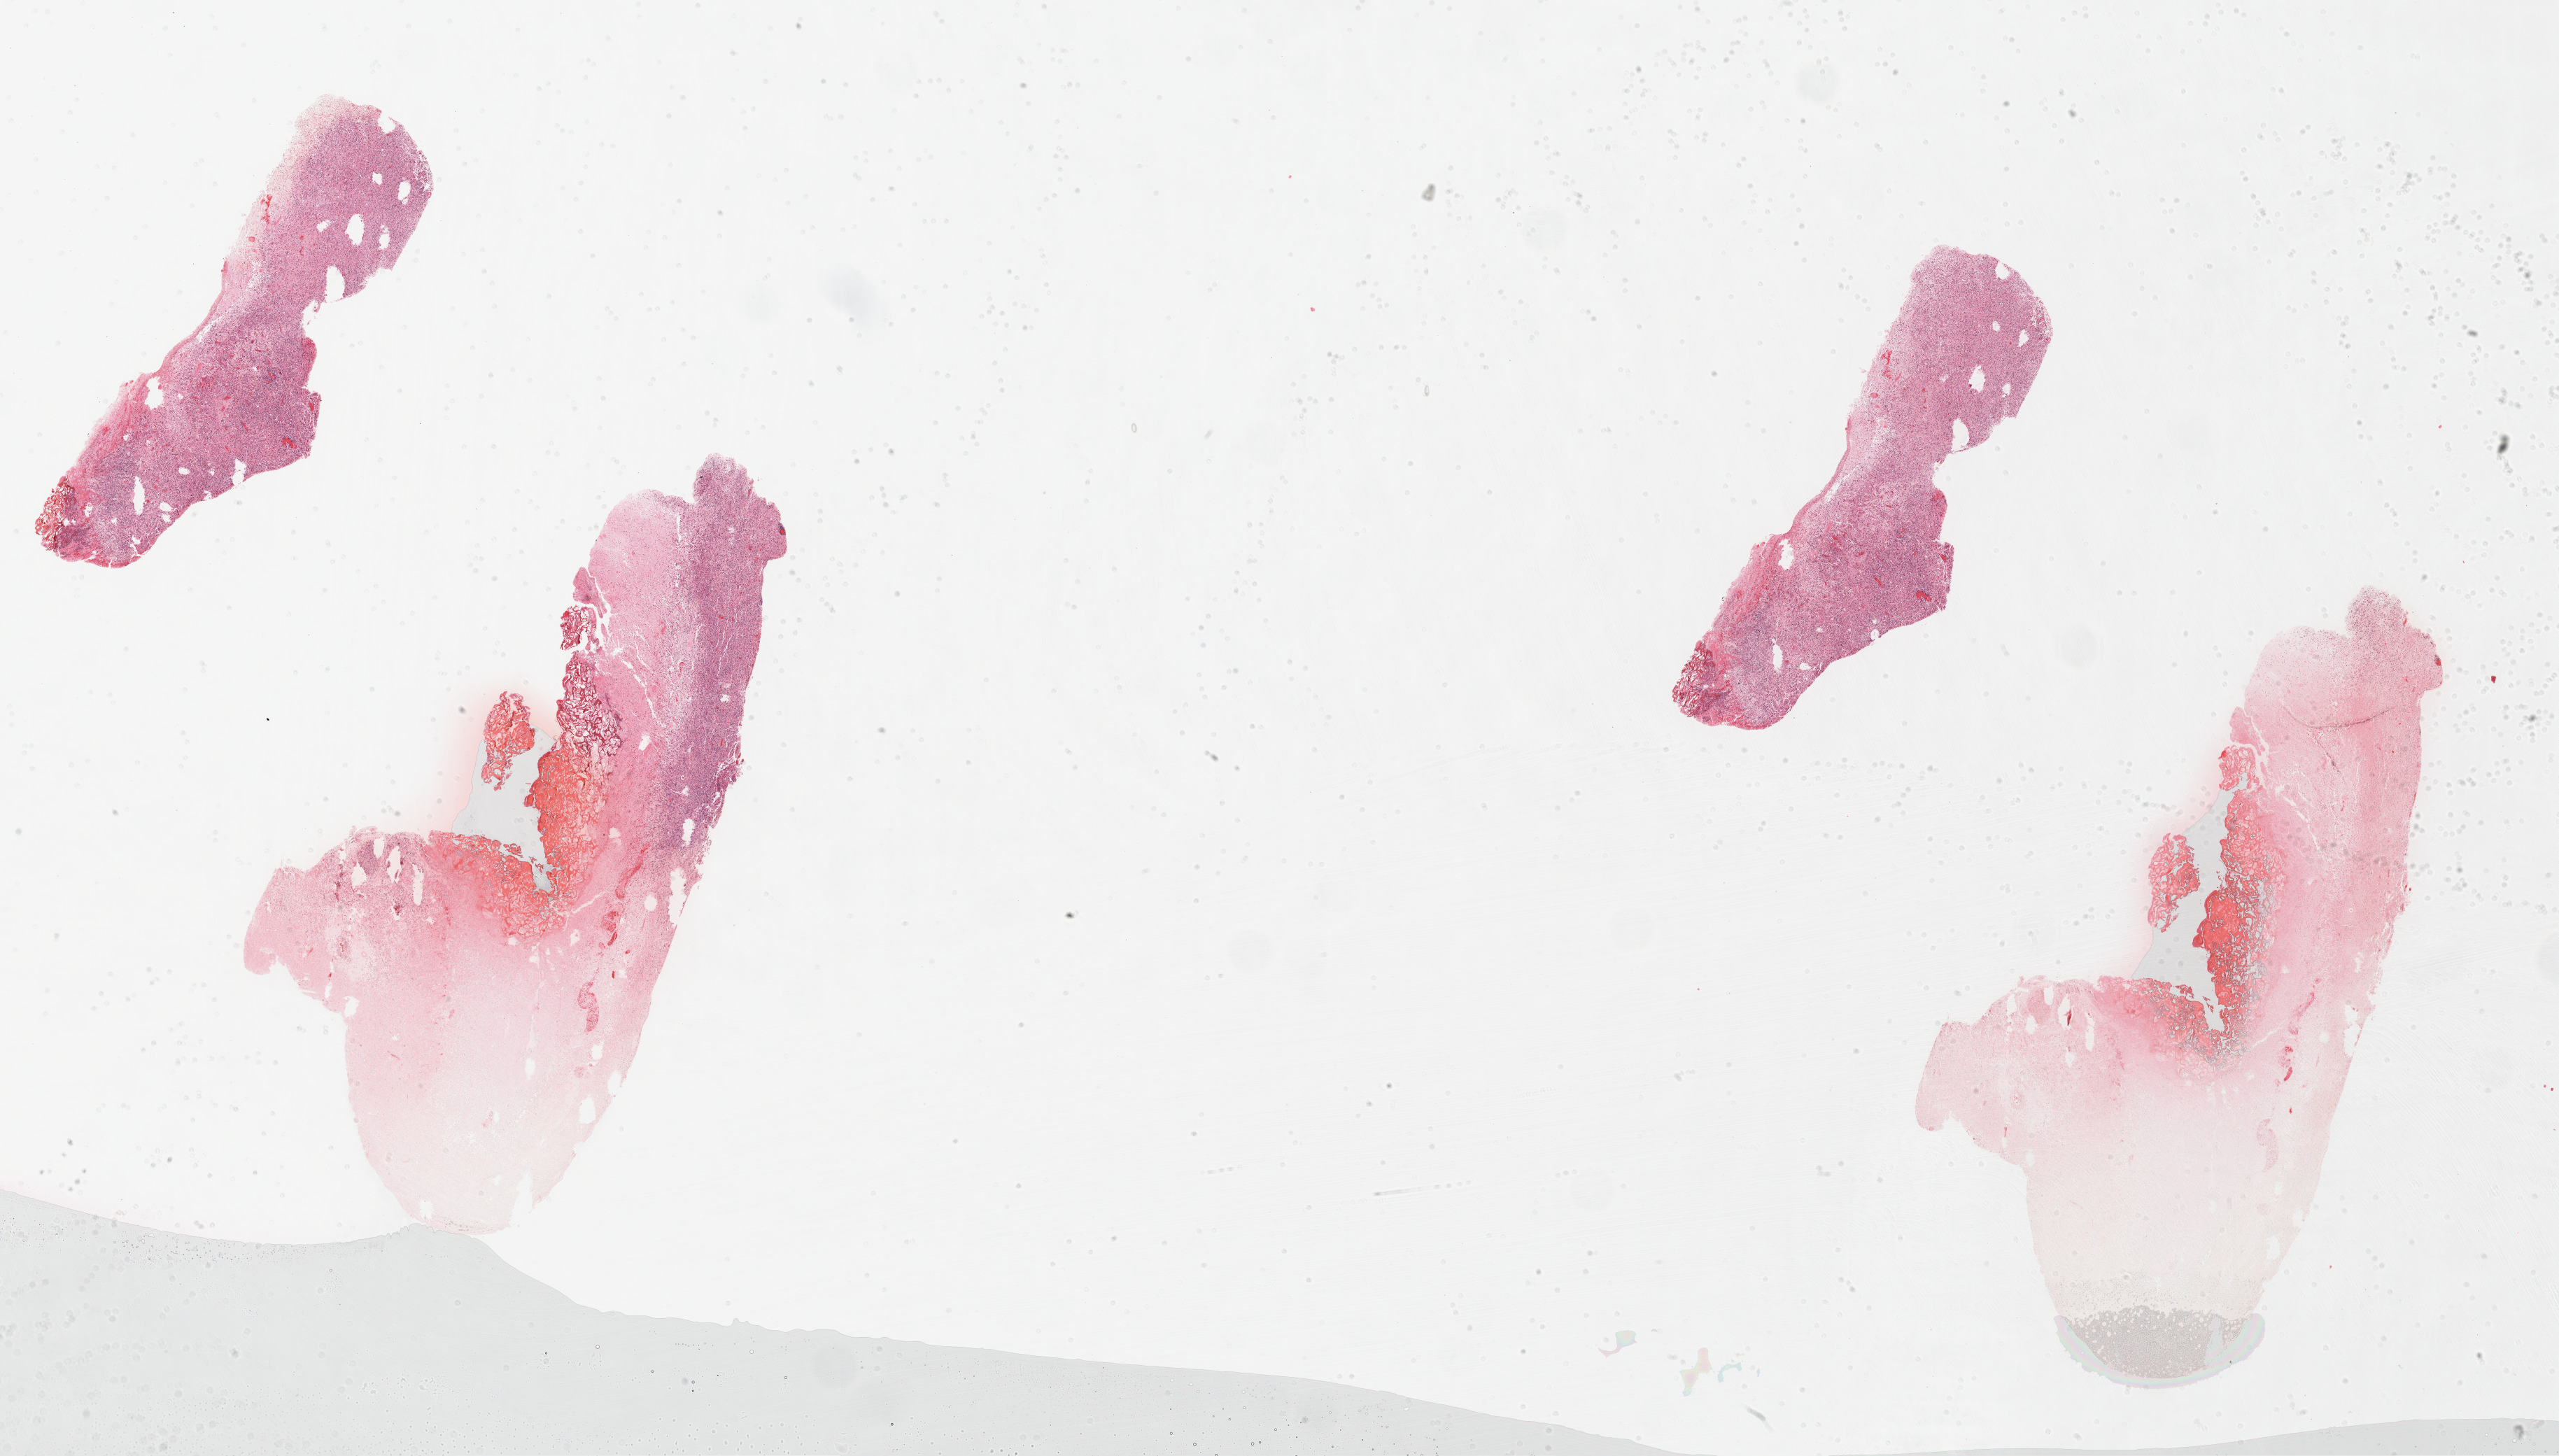
H&E whole-slide image — low-resolution overview of the scanned area, about 29.5 x 16.8 mm. Formalin-fixed paraffin-embedded (FFPE) diagnostic section. Primary tumour sample from the brain. Female, age 51 years at initial diagnosis.
Histologic diagnosis: Glioblastoma.